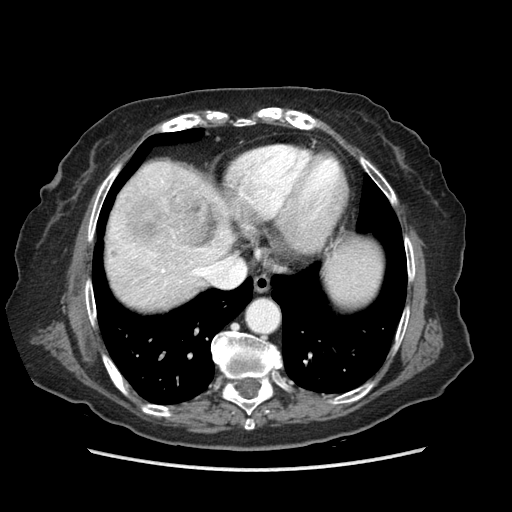
Contrast-enhanced abdominal CT (liver protocol), one axial slice. Soft-tissue window (W 400 / L 40 HU). 512 × 512 image matrix, field of view 360 × 360 mm. From the clinical record (not read from this slice): diagnosis: hepatocellular carcinoma (patient treated with transarterial chemoembolisation; whether this scan precedes or follows treatment is not stated here); TNM stage (as recorded): Stage-IIIA; Child-Pugh class: A; tumour differentiation: well differentiated; tumour size: 11 cm.
Outlined on this slice (semi-automatically segmented with operator editing):
- abdominal aorta: bounding box [x1, y1, x2, y2] px = [248, 301, 278, 331]
- liver parenchyma outside the tumour (the mass and vessels are separate outlines, so this box may not span the whole liver): [106, 160, 378, 308]
- mass: [110, 186, 217, 258]
- liver vessels: [115, 180, 223, 276]